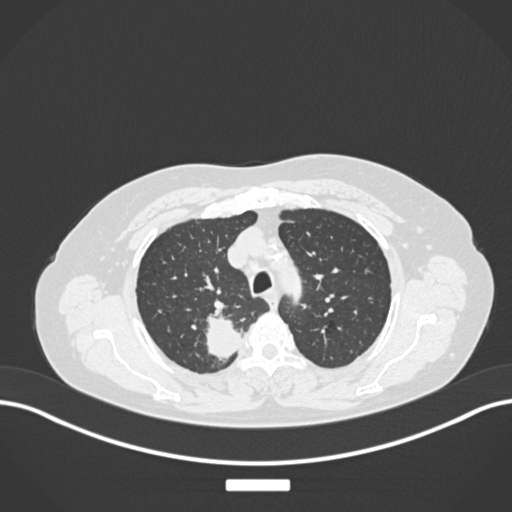
Chest CT, one axial slice; slice 200 of 237 in the series (ordered by position); lung window (W 1500 / L -600 HU); 1 mm slice thickness; 512 × 512 image matrix, field of view 400 × 400 mm. Patient: female, 62 years. From the clinical record (not read from this slice): clinical TNM (as recorded): T1c N1 M0.
Outlined on this slice (bounding box drawn by a radiologist):
- lung tumour (recorded histology: squamous cell carcinoma): bounding box <201,308,245,364> (left, top, right, bottom; pixels)